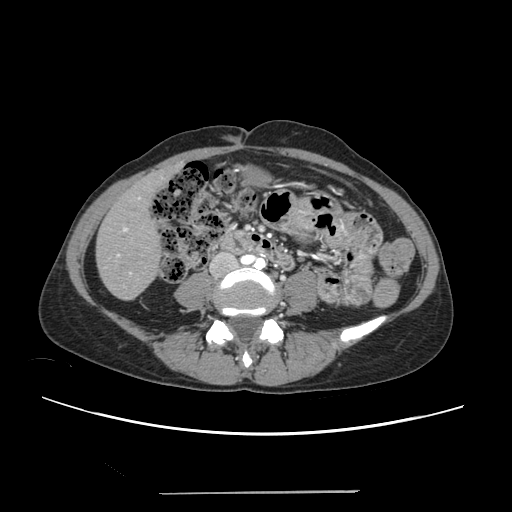
Contrast-enhanced abdominal CT, one axial slice. Position 50 of 240 along the scan axis. 120 kVp. Intravenous contrast given. Soft-tissue window (W 400 / L 40 HU). 512 × 512 image matrix. Female patient, age 60 years. From the clinical record (not read from this slice): diagnosis: colorectal cancer liver metastases, imaged before liver resection; multiple liver metastases: no; largest metastasis: 1.5 cm; disease in both lobes: no.
Structures marked on this image (manually delineated by an expert):
- liver: box from (x=97, y=169) to (x=175, y=299) px
- planned liver remnant (the part of the liver to remain after resection): (x=97, y=171)–(x=169, y=299)
- portal vein (with intrahepatic branches): (x=115, y=196)–(x=141, y=274)